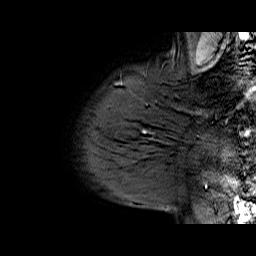
Breast MRI (dynamic contrast-enhanced), one sagittal slice; position 57 of 70 along the scan axis; dynamic contrast-enhanced series, time point 2 of 6 at this slice position (early post-contrast); 1.5 T; TE 6.5 ms, TR 33 ms; 4 mm slice thickness; 256 × 256 image matrix. Female patient. From the clinical record (not read from this slice): setting: breast cancer imaged before/during neoadjuvant chemotherapy; receptor status: HER2-positive.
Structures marked on this image (semi-automatically segmented with operator editing):
- analysis volume of interest (the breast-tissue region the enhancement analysis was run in; not a lesion): bounding box [x1, y1, x2, y2] px = [113, 112, 174, 170]
- tumour enhancement mask (voxels above the 100 % enhancement threshold inside the analysis volume of interest): [142, 130, 147, 133]